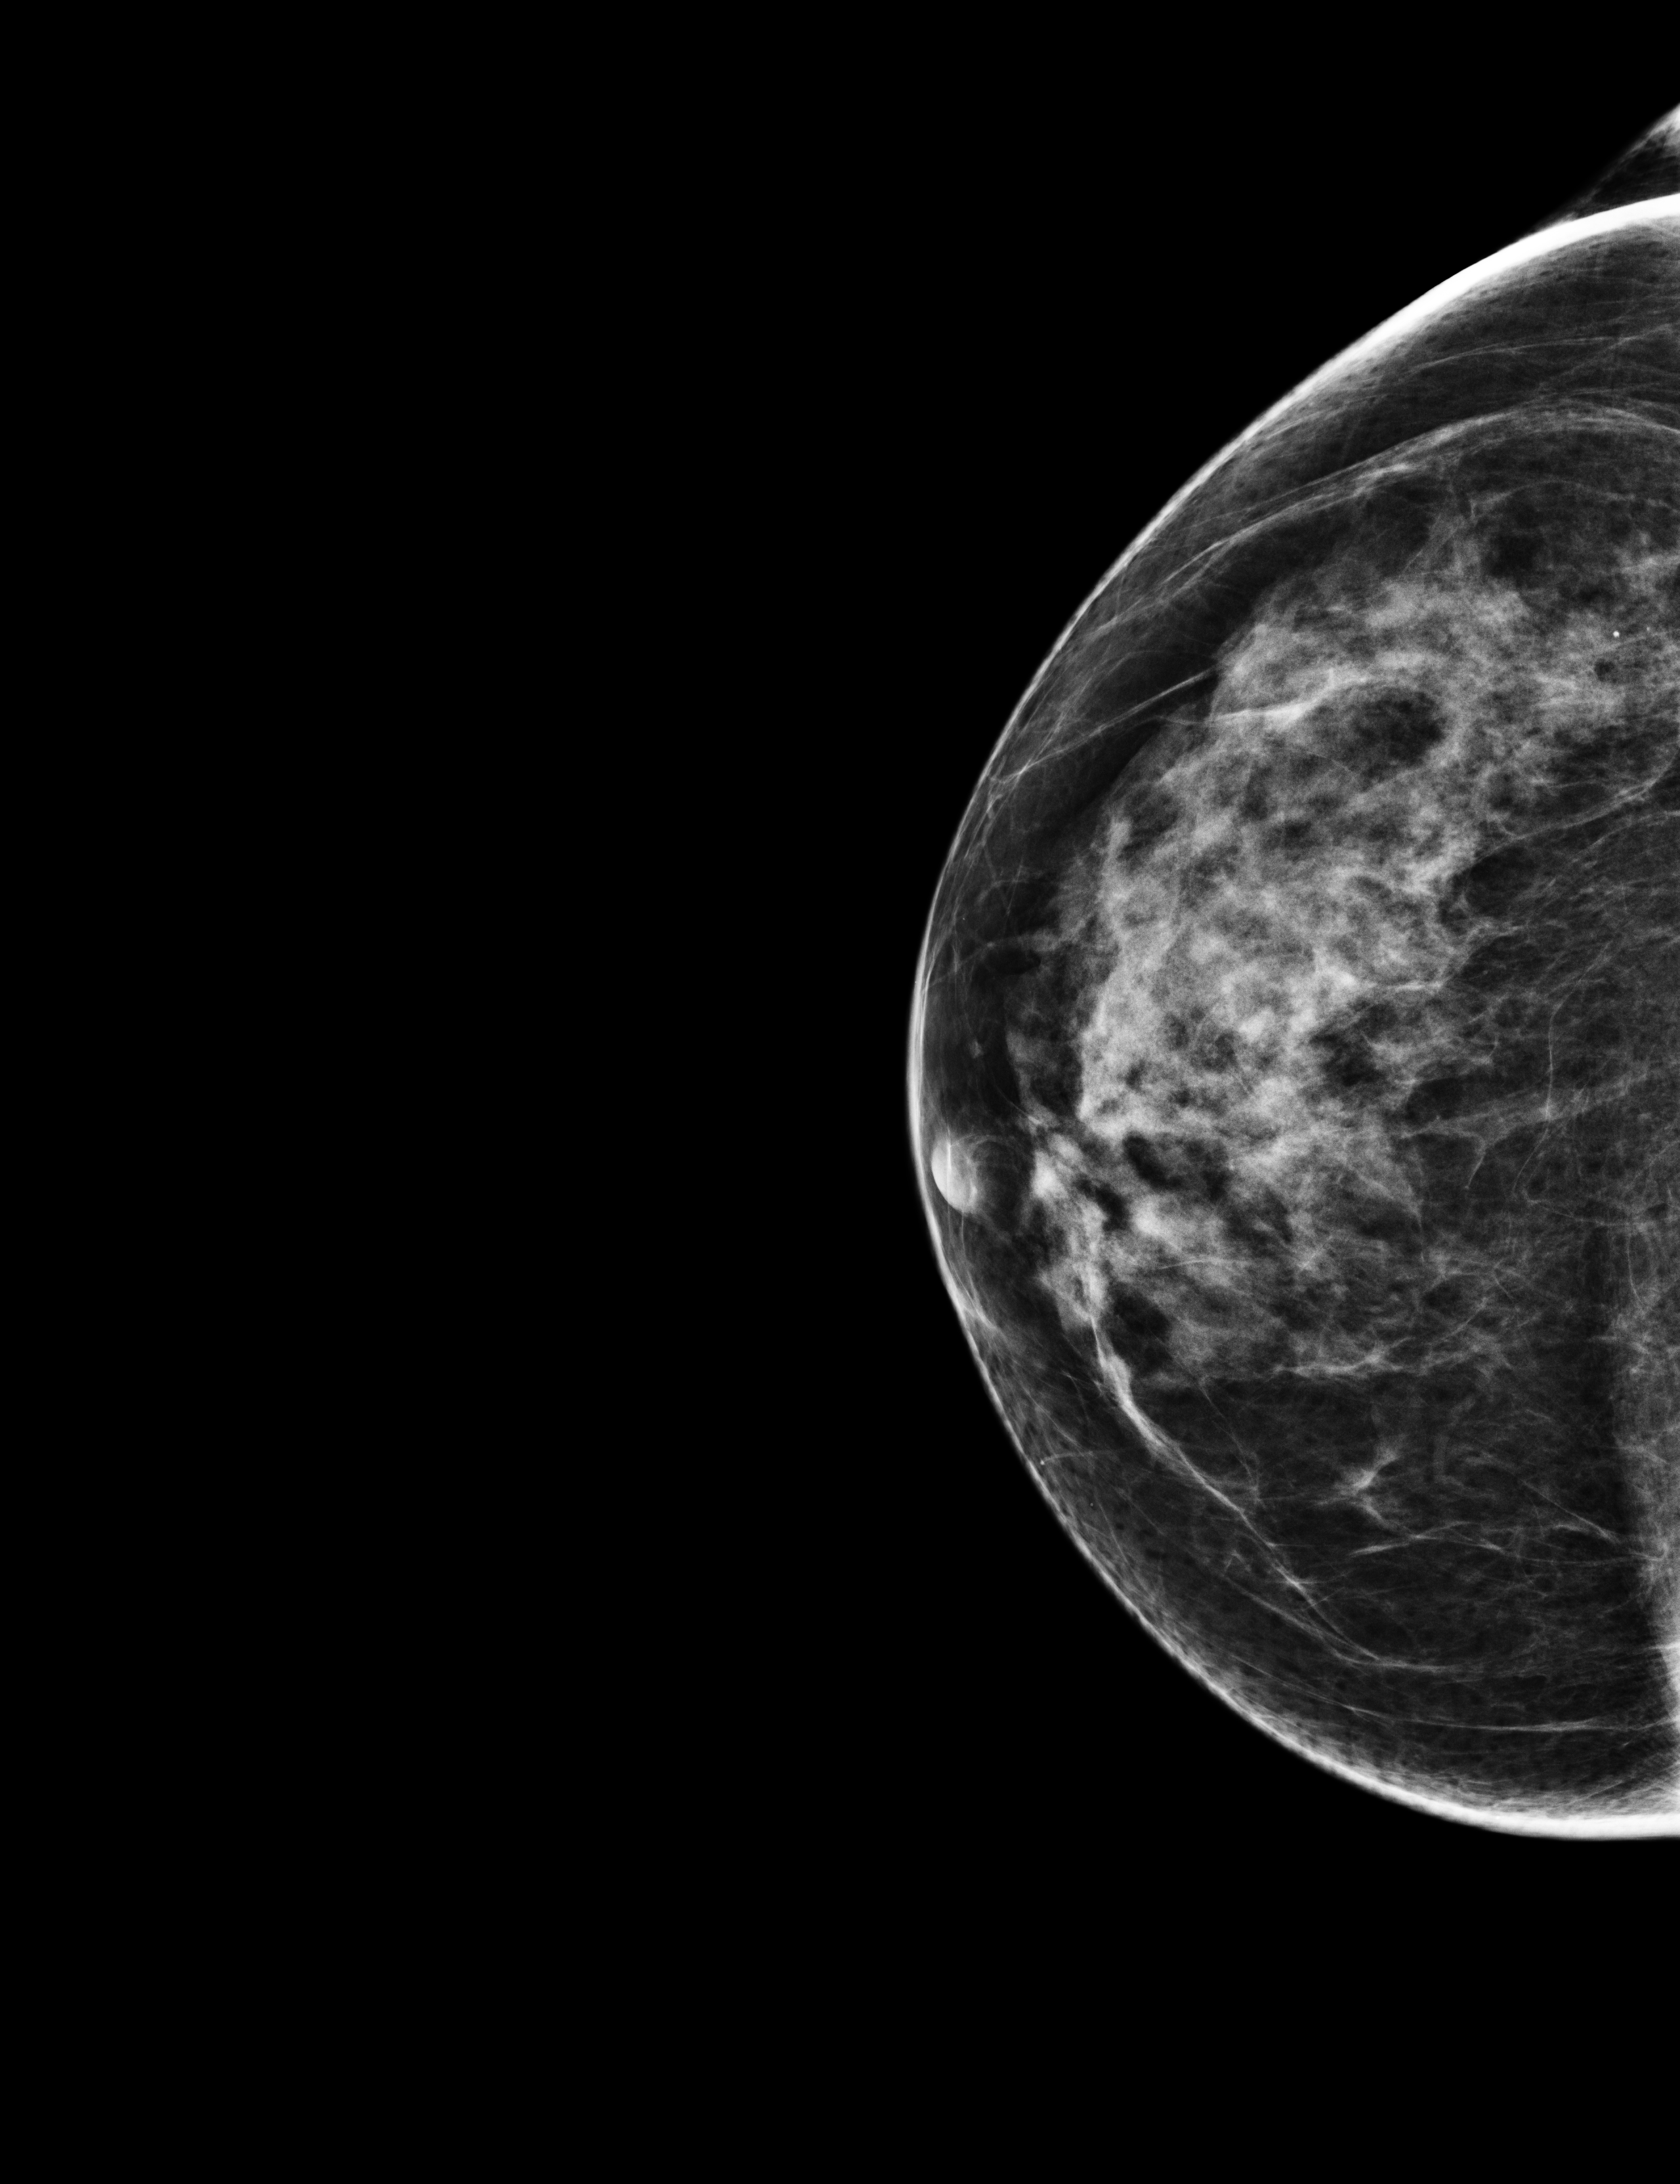
Screening examination; compressed breast thickness 56 mm; system: Selenia Dimensions.
Image type: full-field digital mammogram. Breast: right. Projection: CC view.